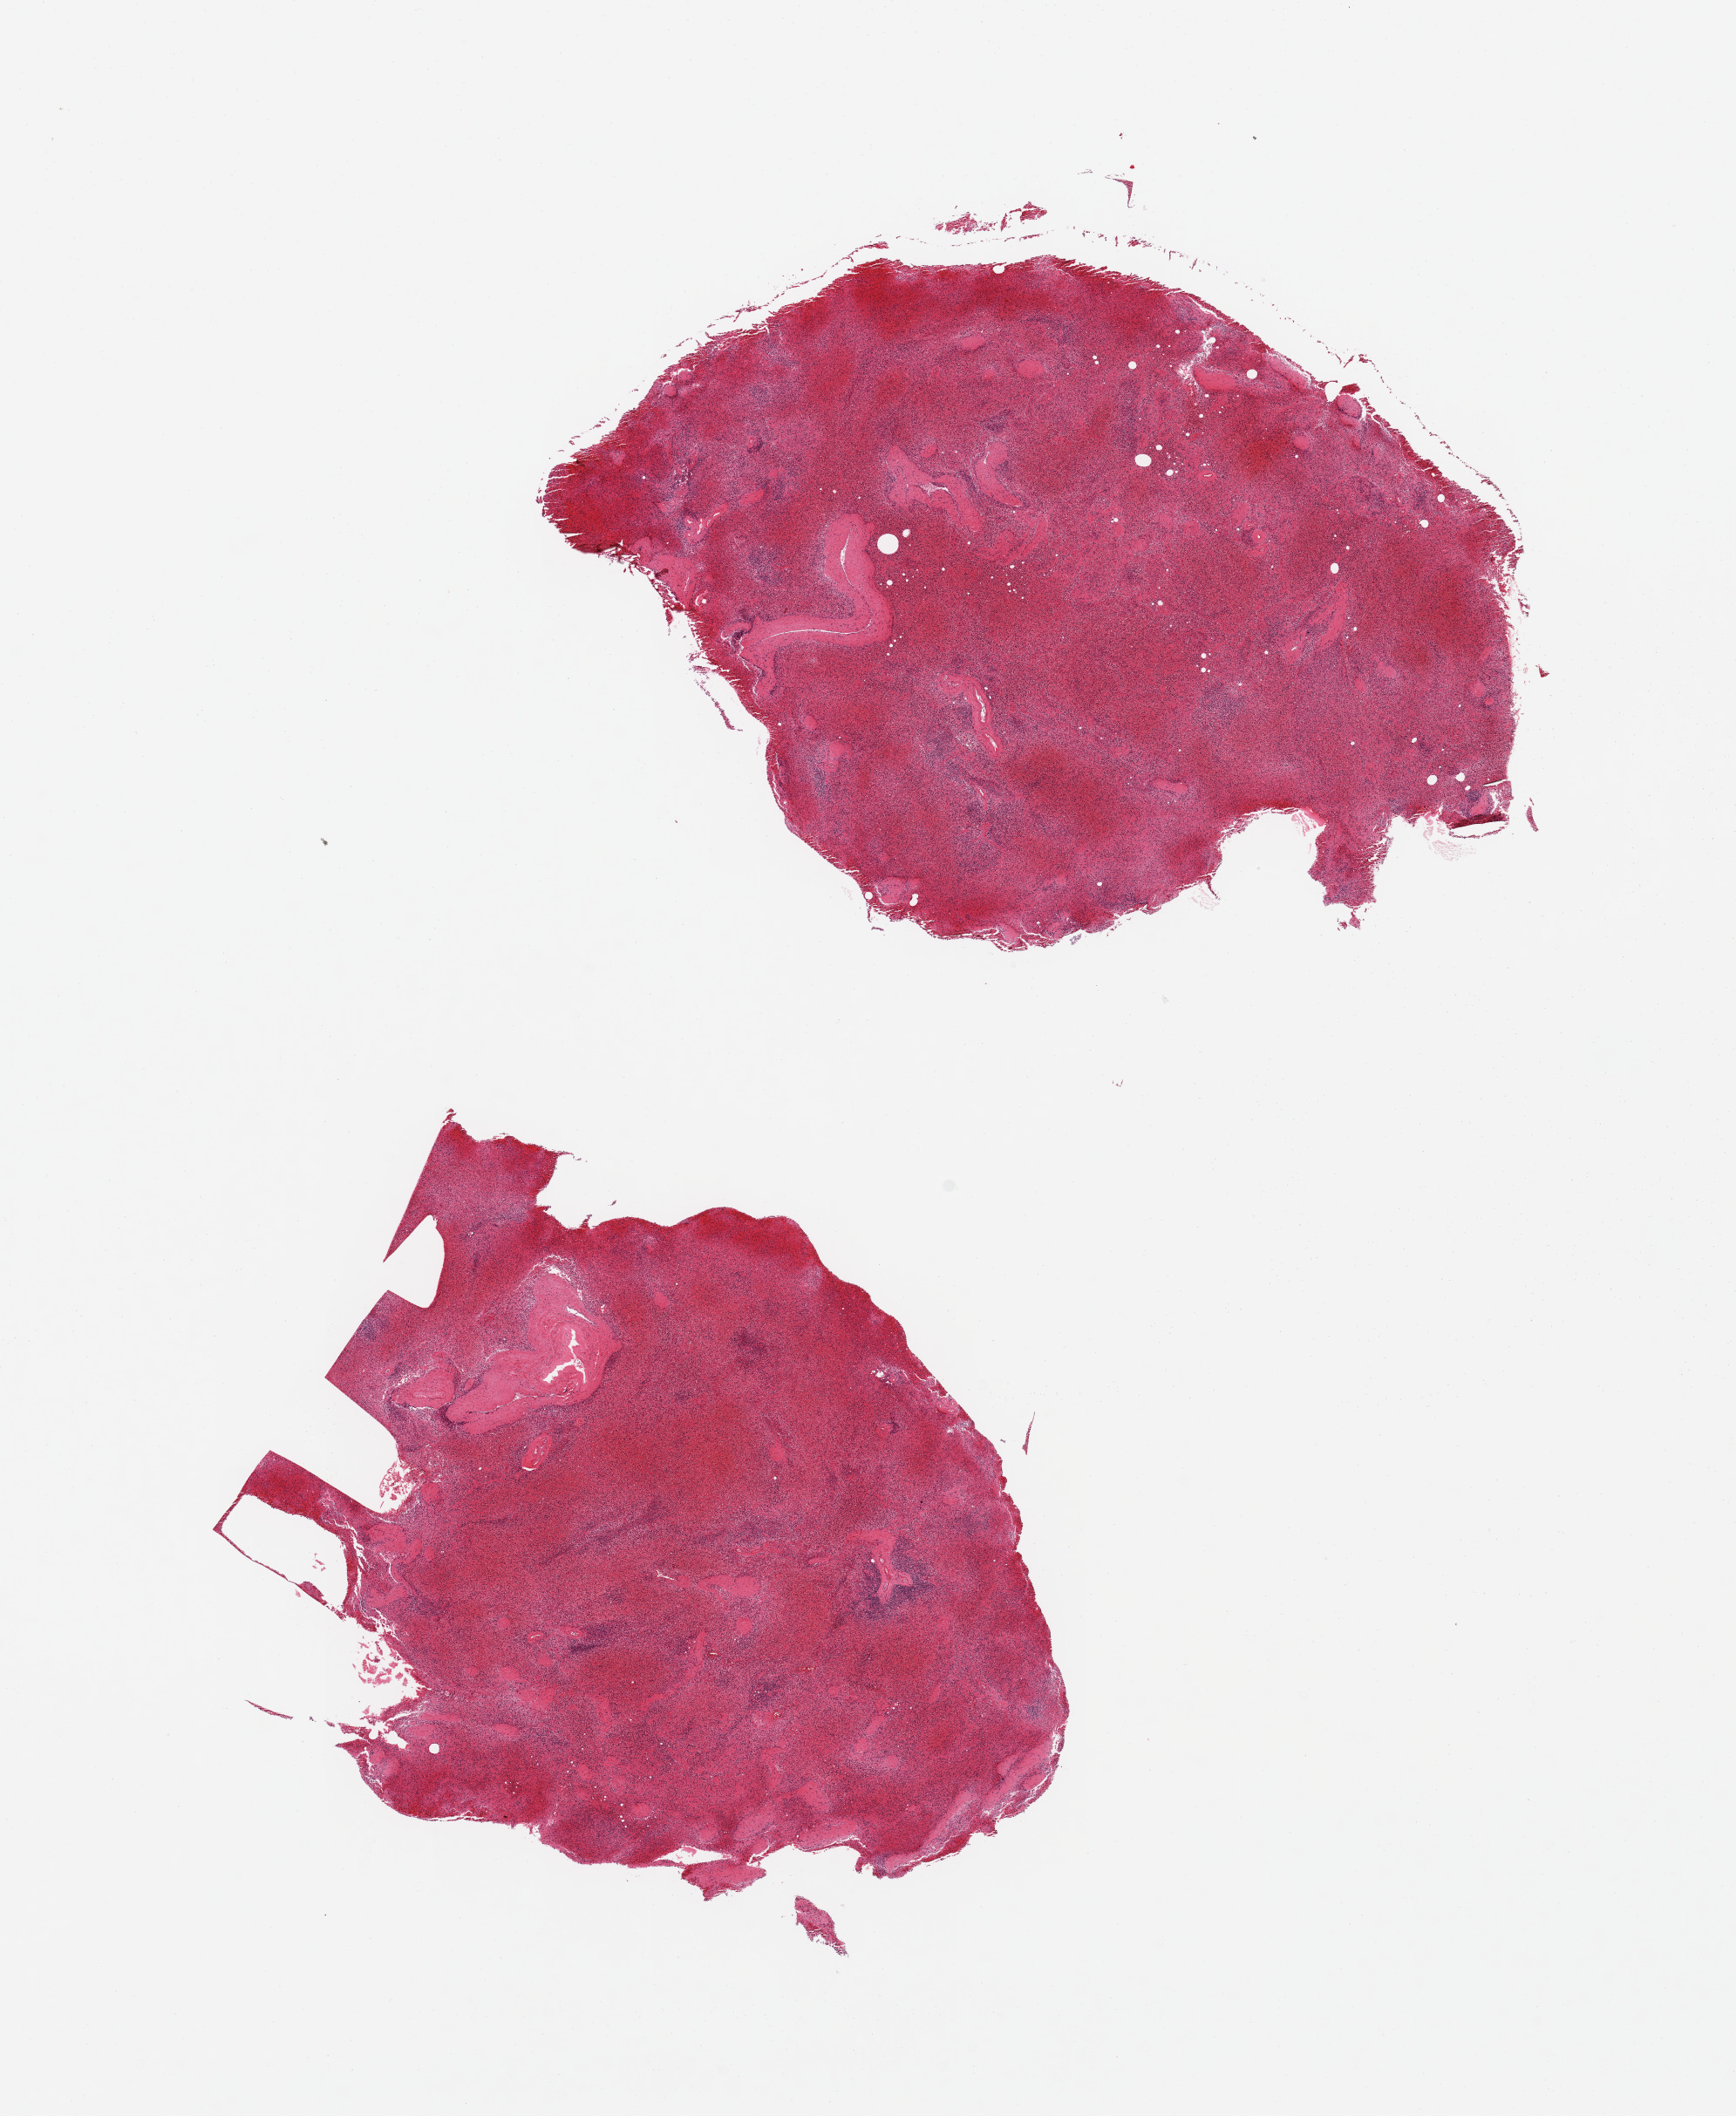
Haematoxylin and eosin whole-slide image — shown as a low-resolution overview of the whole scanned area (about 15.8 x 19.2 mm), PAXgene-fixed, paraffin-embedded tissue, section of spleen (target tissue), donor tissue sample. Donor sex: female.
Pathologist's review note for this sample: 2 pieces, marked autolysis, congested.